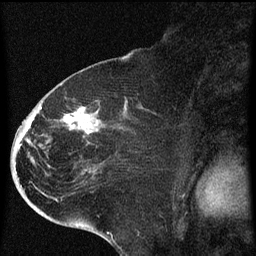
Breast MRI (dynamic contrast-enhanced), one sagittal slice. Position 33 of 60 along the scan axis. Dynamic contrast-enhanced series, image 2 of 4 at this slice position (ordered by acquisition). 1.5 T. TE 4.2 ms, TR 8 ms. 2 mm slice thickness. 256 × 256 image matrix, field of view 180 × 180 mm. Patient: female, 71 years.
Outlined on this slice (semi-automatically segmented with operator editing):
- analysis volume of interest (the breast-tissue region the enhancement analysis was run in; not a lesion): box from (x=32, y=86) to (x=141, y=205) px
- tumour enhancement mask (voxels above the 70 % enhancement threshold inside the analysis volume of interest): (x=39, y=98)–(x=98, y=137)